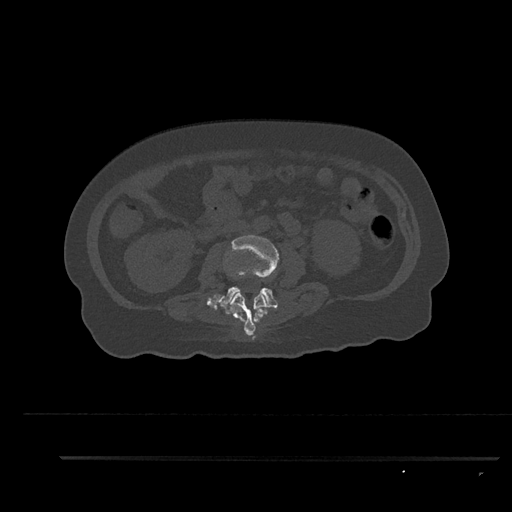
CT including the spine, one axial slice; slice 119 of 797 in the series (ordered by position); reconstruction kernel Br40s/3; 120 kVp; bone window (W 1800 / L 400 HU); 512 × 512 image matrix, field of view 408 × 408 mm. Female patient, age 44 years. From the clinical record (not read from this slice): primary cancer: renal; vertebrae with lytic lesions (as recorded): L1.
Outlined on this slice (semi-automatic segmentation, software-assisted and operator-edited):
- L2 vertebra: bounding box (x1, y1, x2, y2) in pixels: (224, 293, 269, 336)
- L3 vertebra: (218, 235, 280, 308)